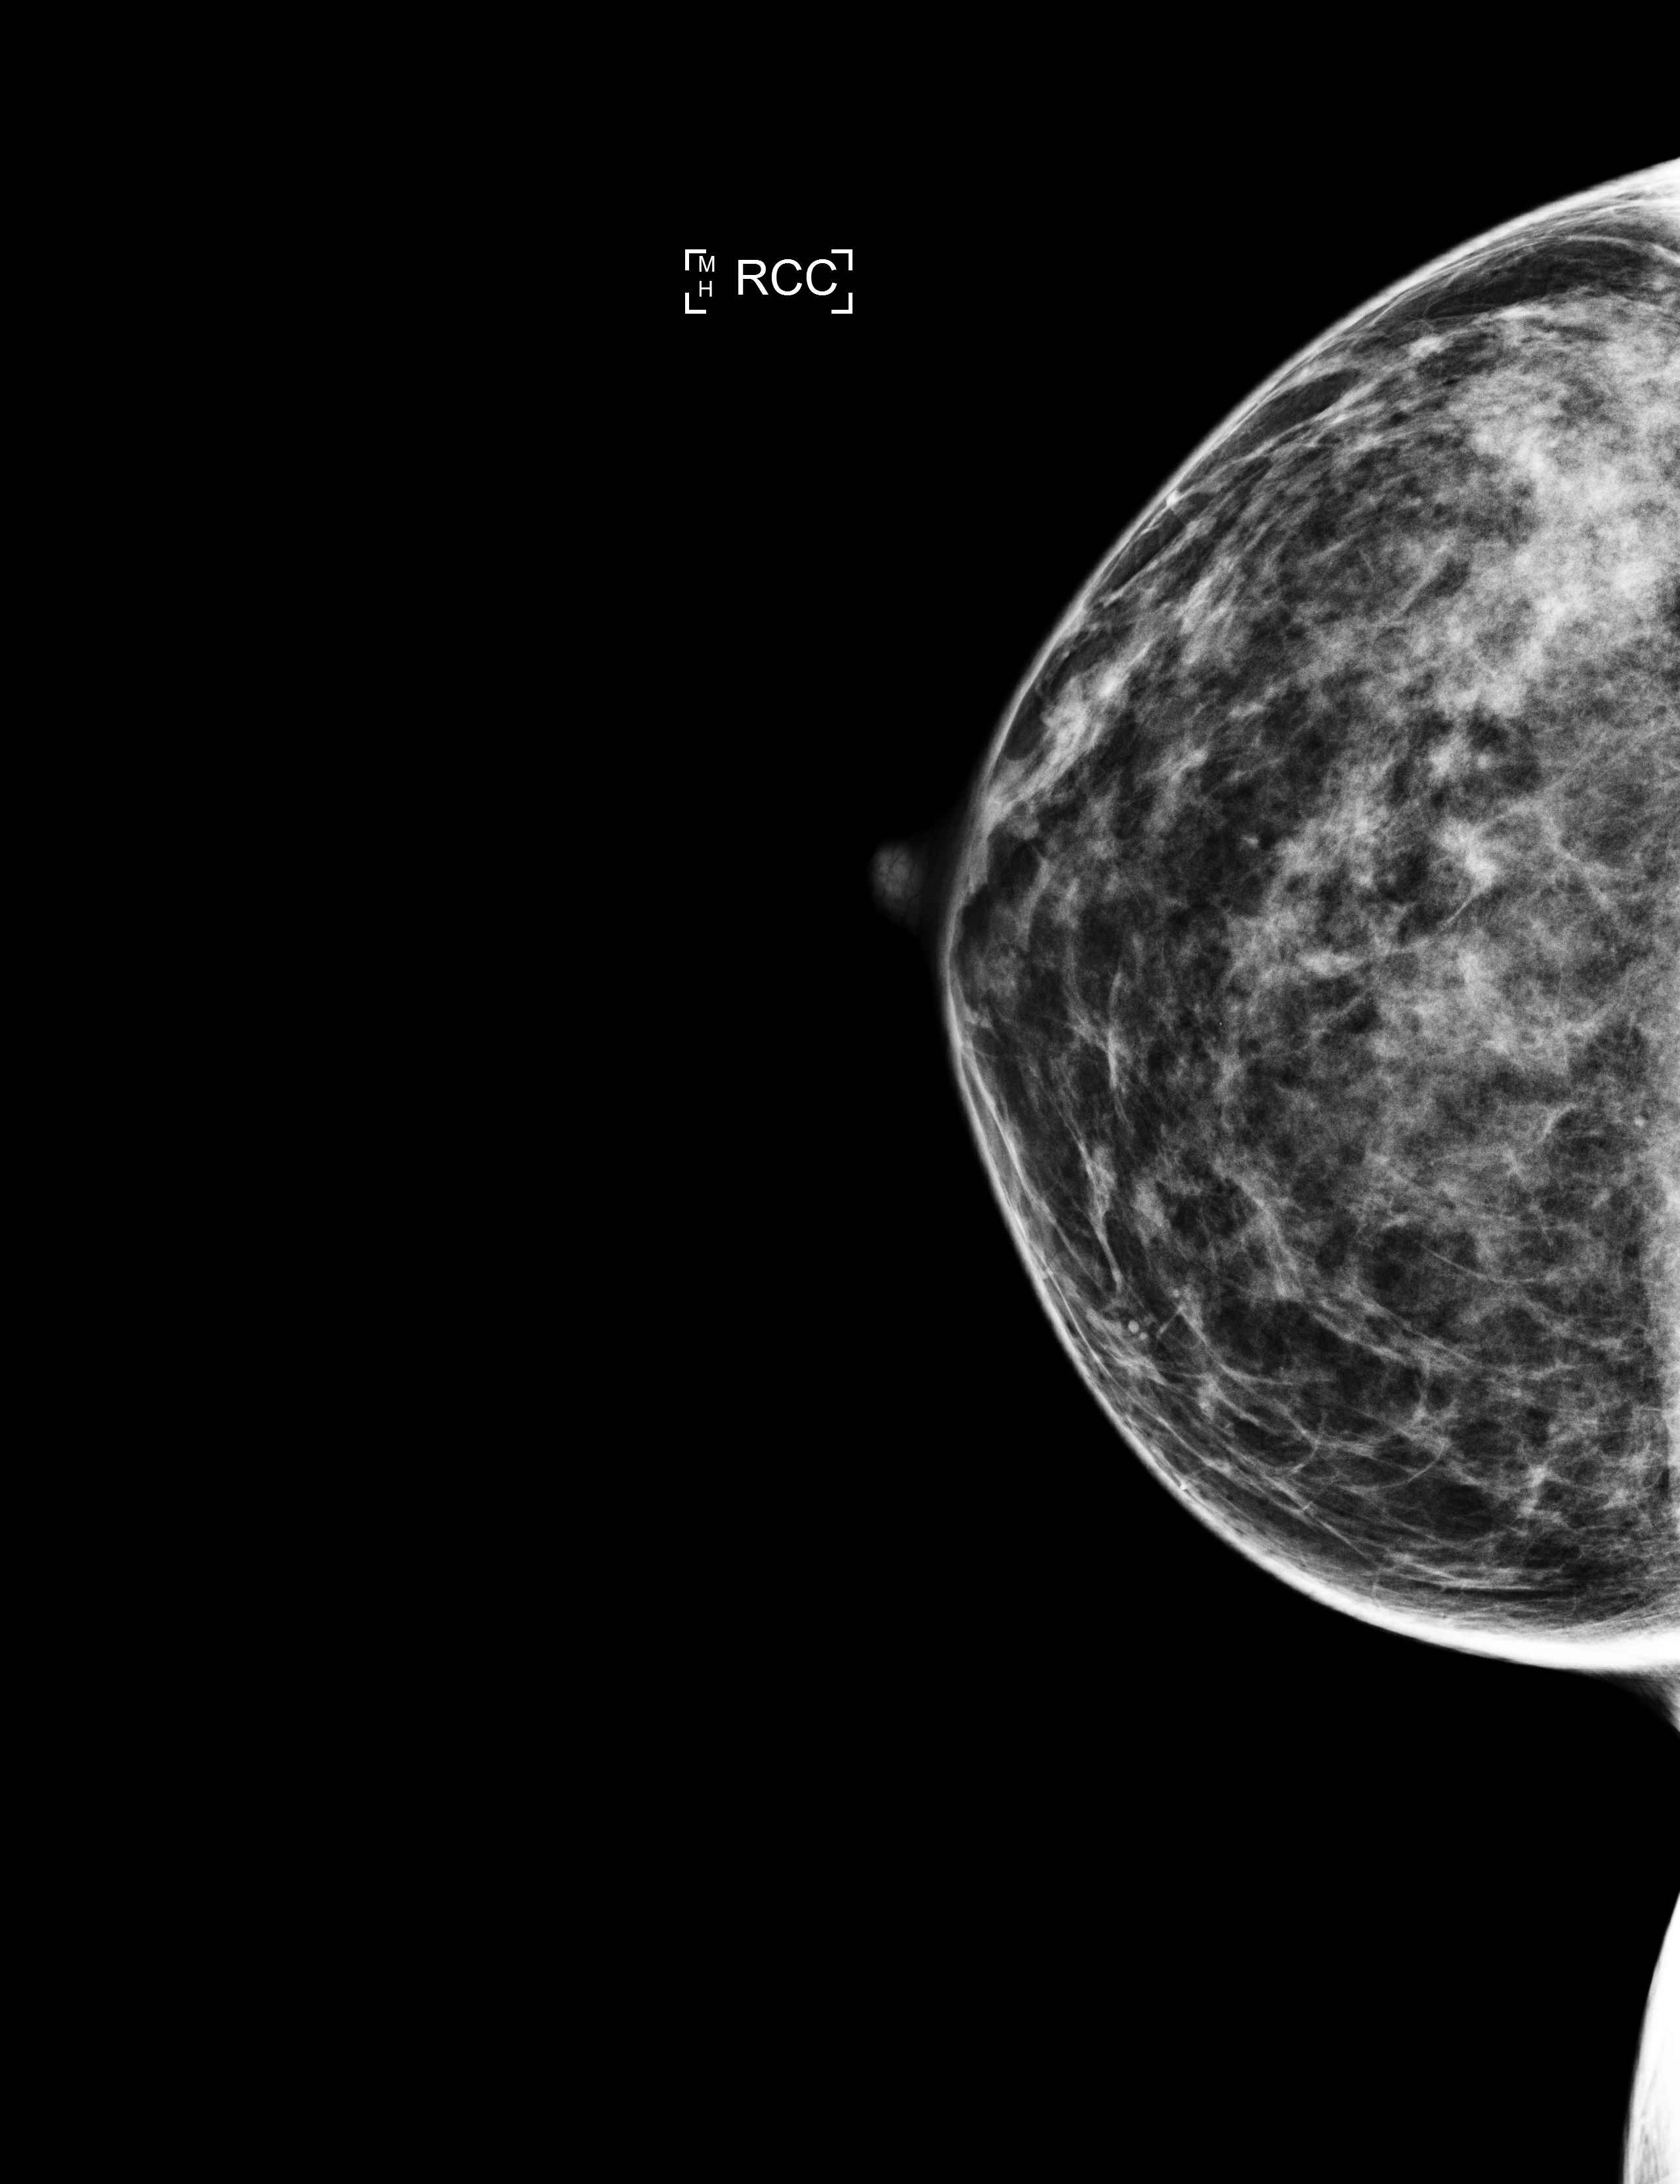
Annual screening mammography examination, system: Selenia Dimensions. Patient: female, 42 years.
Image type: full-field digital mammogram. Breast: right. Projection: cranio-caudal projection.